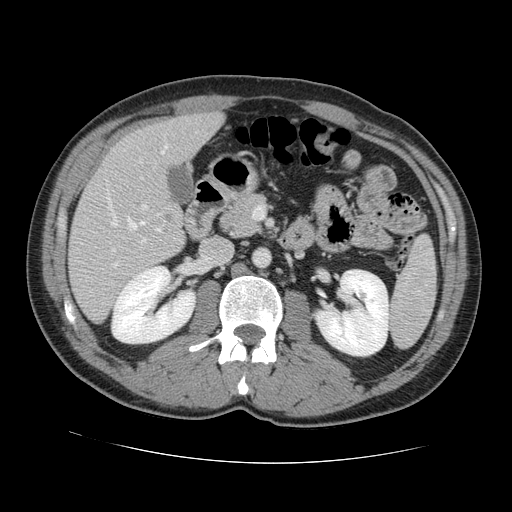
Contrast-enhanced abdominal CT, one axial slice; position 62 of 131 along the scan axis; soft-tissue window (W 400 / L 40 HU); 512 × 512 image matrix, field of view 380 × 380 mm. Male patient, age 40 years. Case-level facts recorded for this patient, not image findings: diagnosis: colorectal cancer liver metastases, imaged before liver resection; multiple liver metastases: yes; largest metastasis: 2.9 cm; chemotherapy before resection: yes.
Structures marked on this image (expert manual segmentation):
- hepatic veins: bounding box [x1, y1, x2, y2] px = [108, 144, 169, 251]
- liver: [69, 114, 221, 321]
- planned liver remnant (the part of the liver to remain after resection): [110, 114, 221, 179]
- portal vein (with intrahepatic branches): [113, 177, 162, 267]
- liver metastasis: [165, 216, 173, 222]